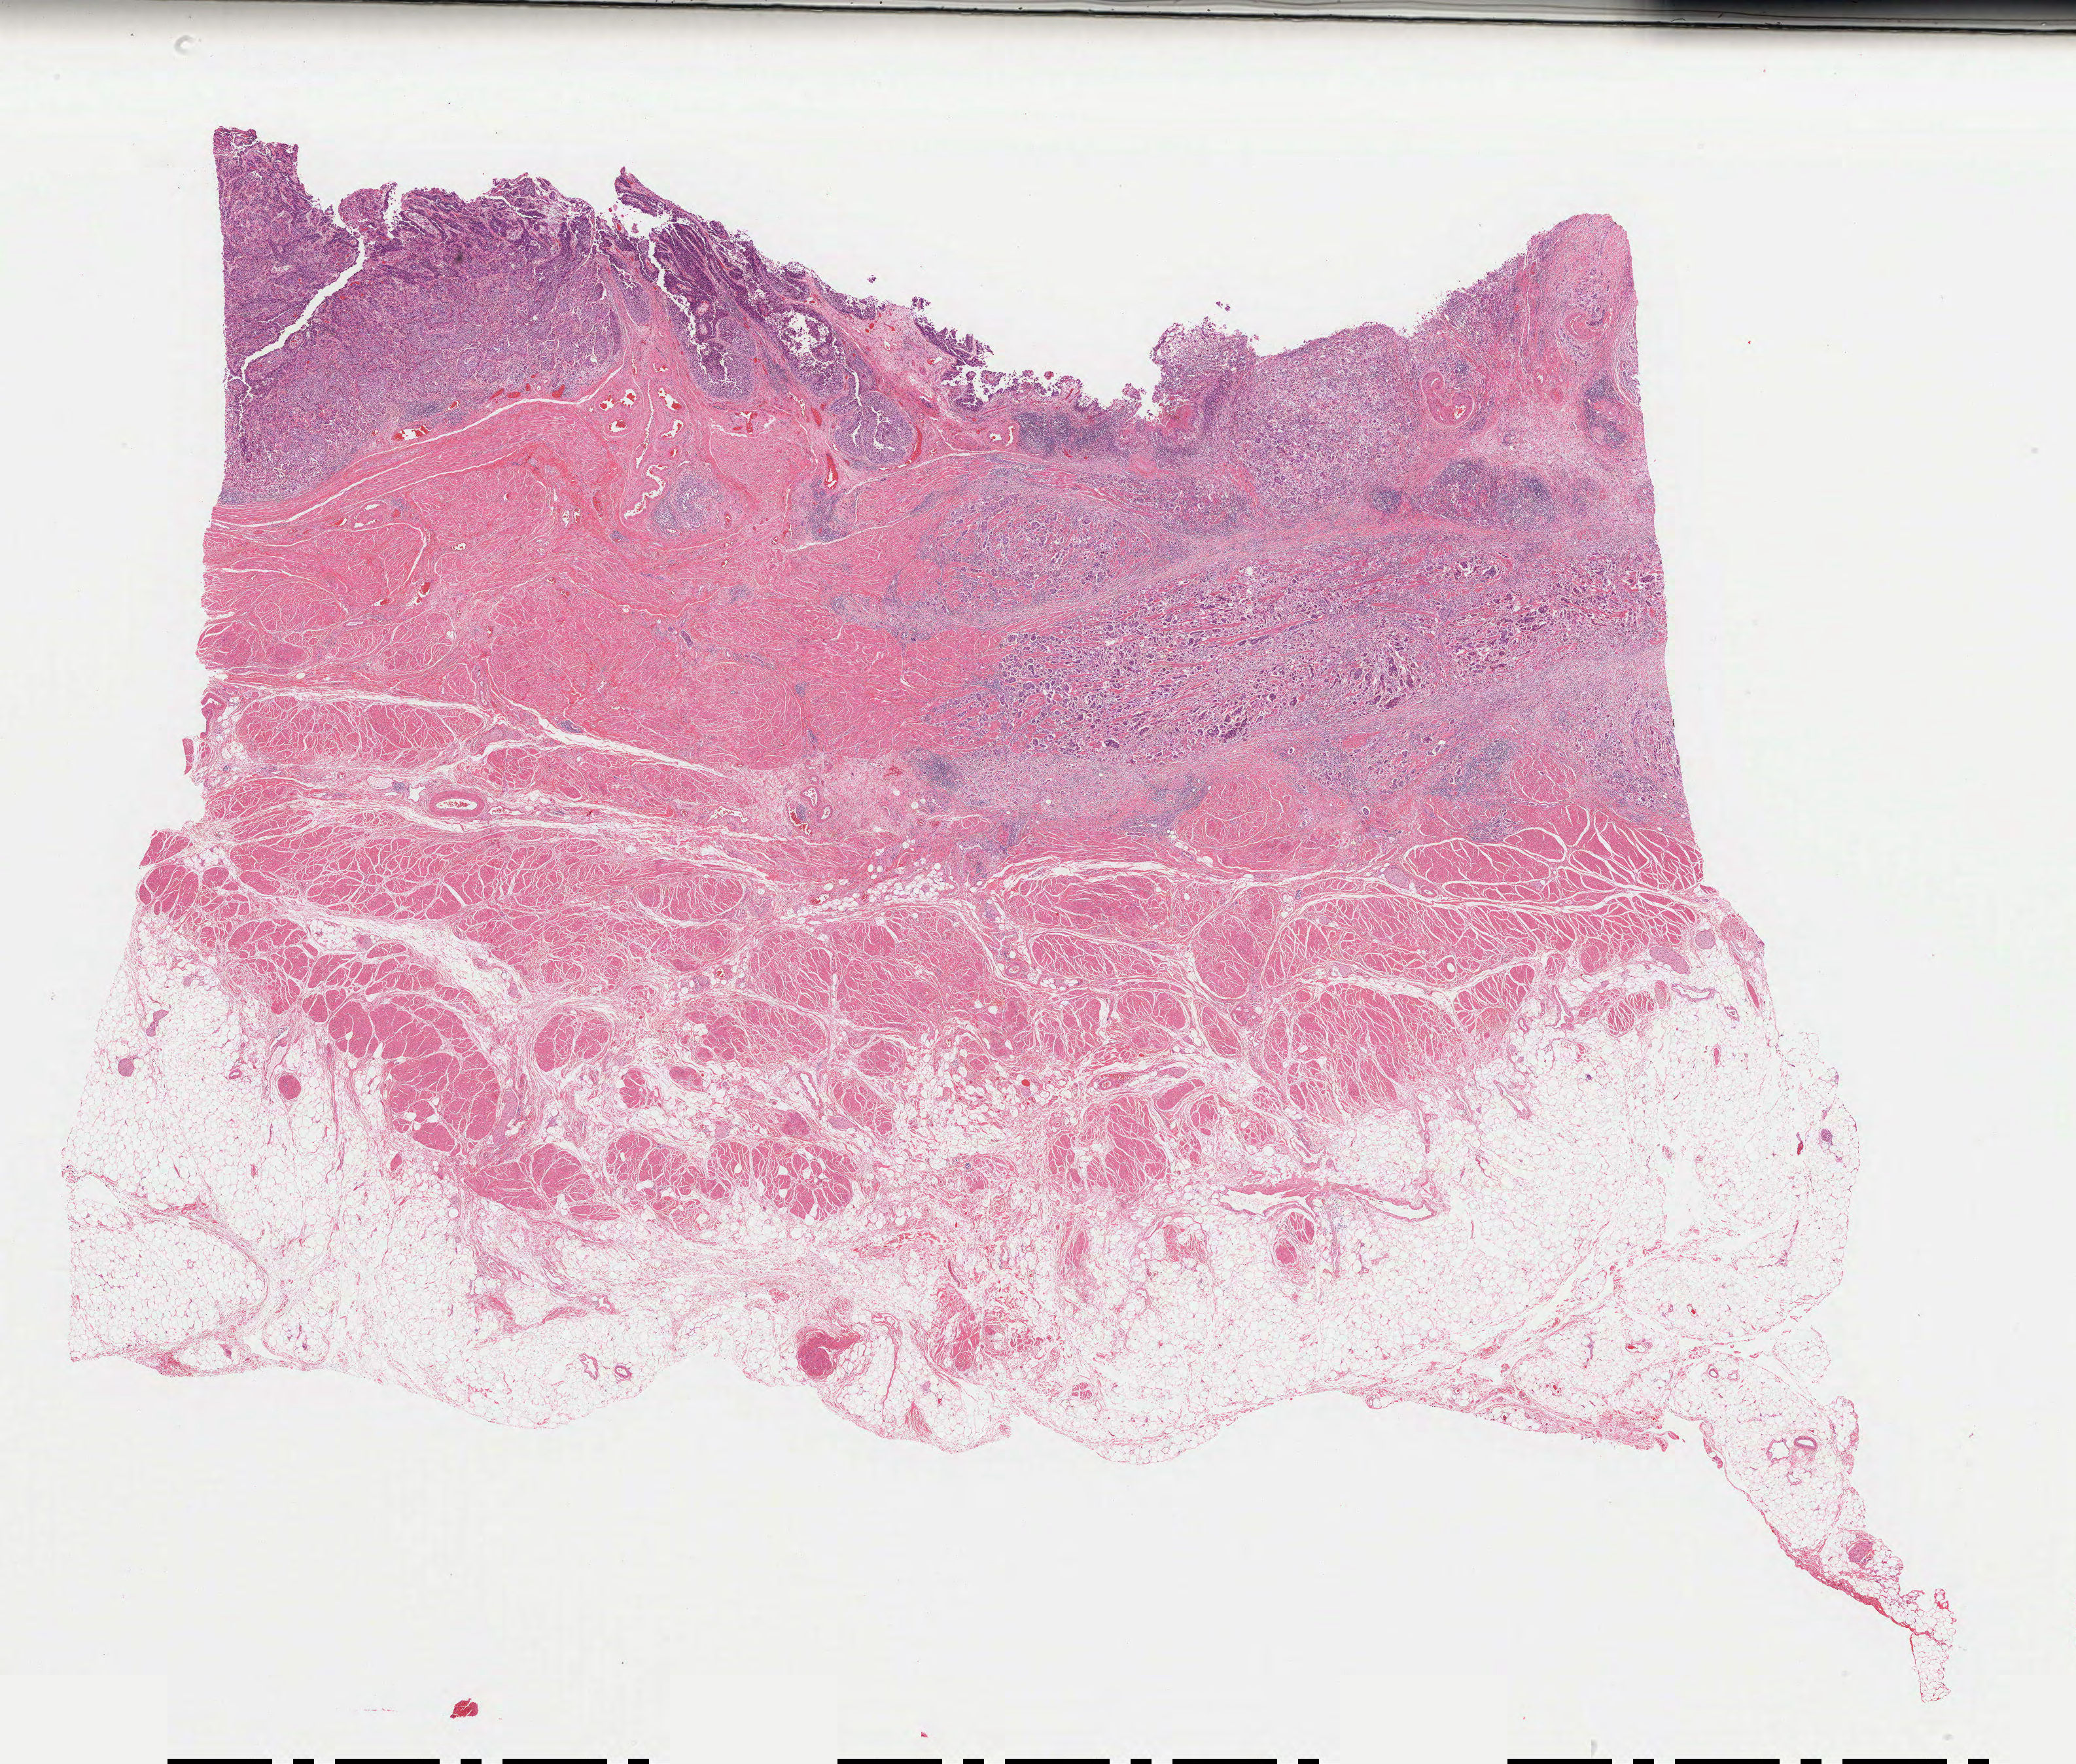
Digitized H&E-stained tissue section (whole slide) — whole scanned area (about 25.2 x 21.4 mm) shown as a low-resolution overview; formalin-fixed paraffin-embedded (FFPE) diagnostic section; bladder, primary tumour sample. Patient: male, age at initial diagnosis 66 years. Histologic grade: high grade.
* pathologic diagnosis: Transitional cell carcinoma
* lymph nodes positive (case pathology): 1 of 17 examined
* AJCC pathologic stage: IV (7th edition)